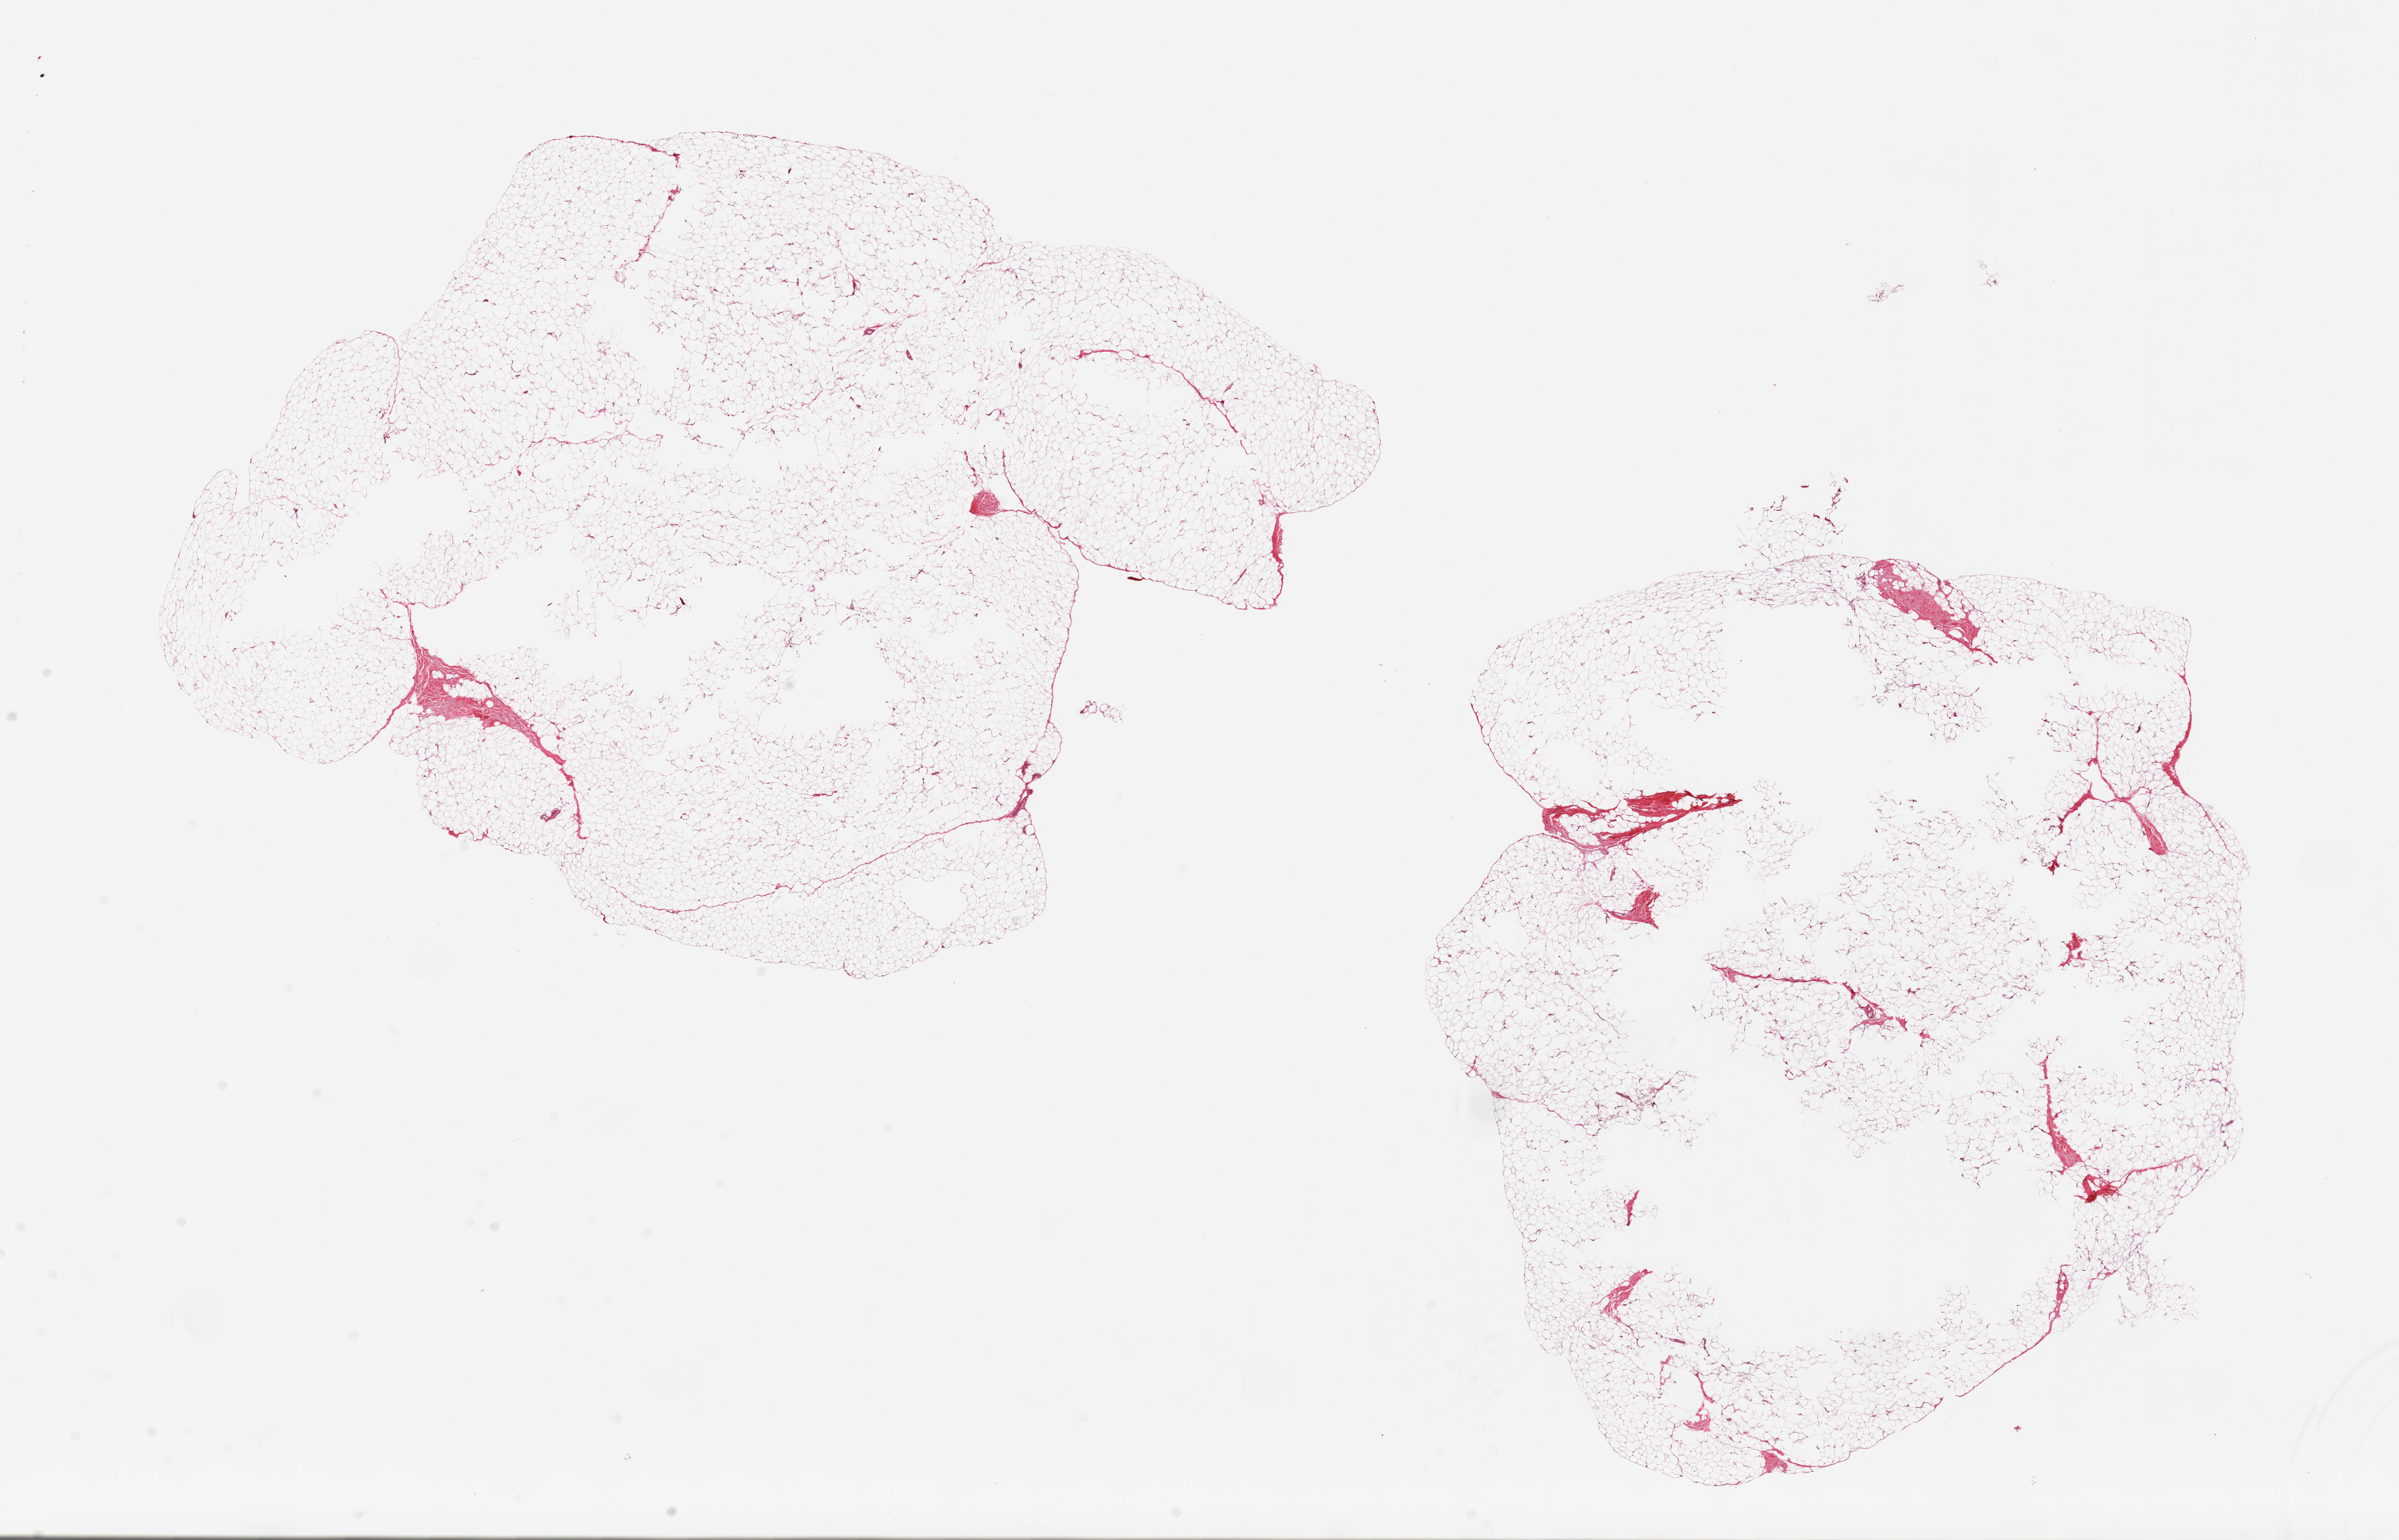
Digitized H&E-stained section — whole scanned area (about 27.6 x 17.7 mm, slide scanned at 20x) shown as a low-resolution overview. PAXgene-fixed, paraffin-embedded tissue. Section of breast (target tissue). Donor tissue sample. Donor sex: male.
Pathologist's review note for this sample: 2 pieces, fibroadipose tissue, no ductal elements.